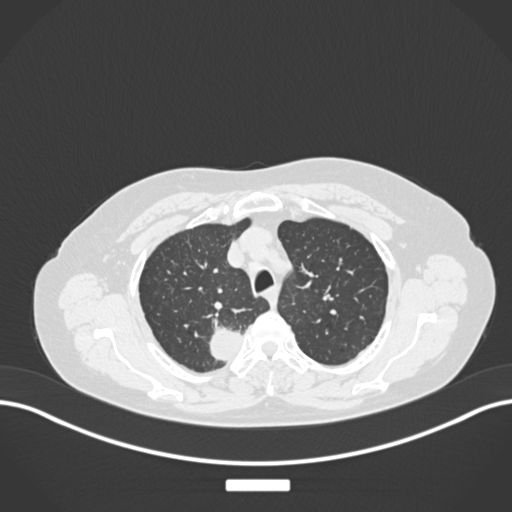
Chest CT, one axial slice. Slice 206 of 237 in the series (ordered by position). Reconstruction kernel B30f. 120 kVp. Lung window (W 1500 / L -600 HU). 512 × 512 image matrix. Female patient, age 62 years. Case-level facts recorded for this patient, not image findings: clinical TNM (as recorded): T1c N1 M0.
Outlined on this slice (rectangle marked by the reading radiologist):
- lung tumour (recorded histology: squamous cell carcinoma): bounding box (x1, y1, x2, y2) in pixels: (201, 318, 255, 369)